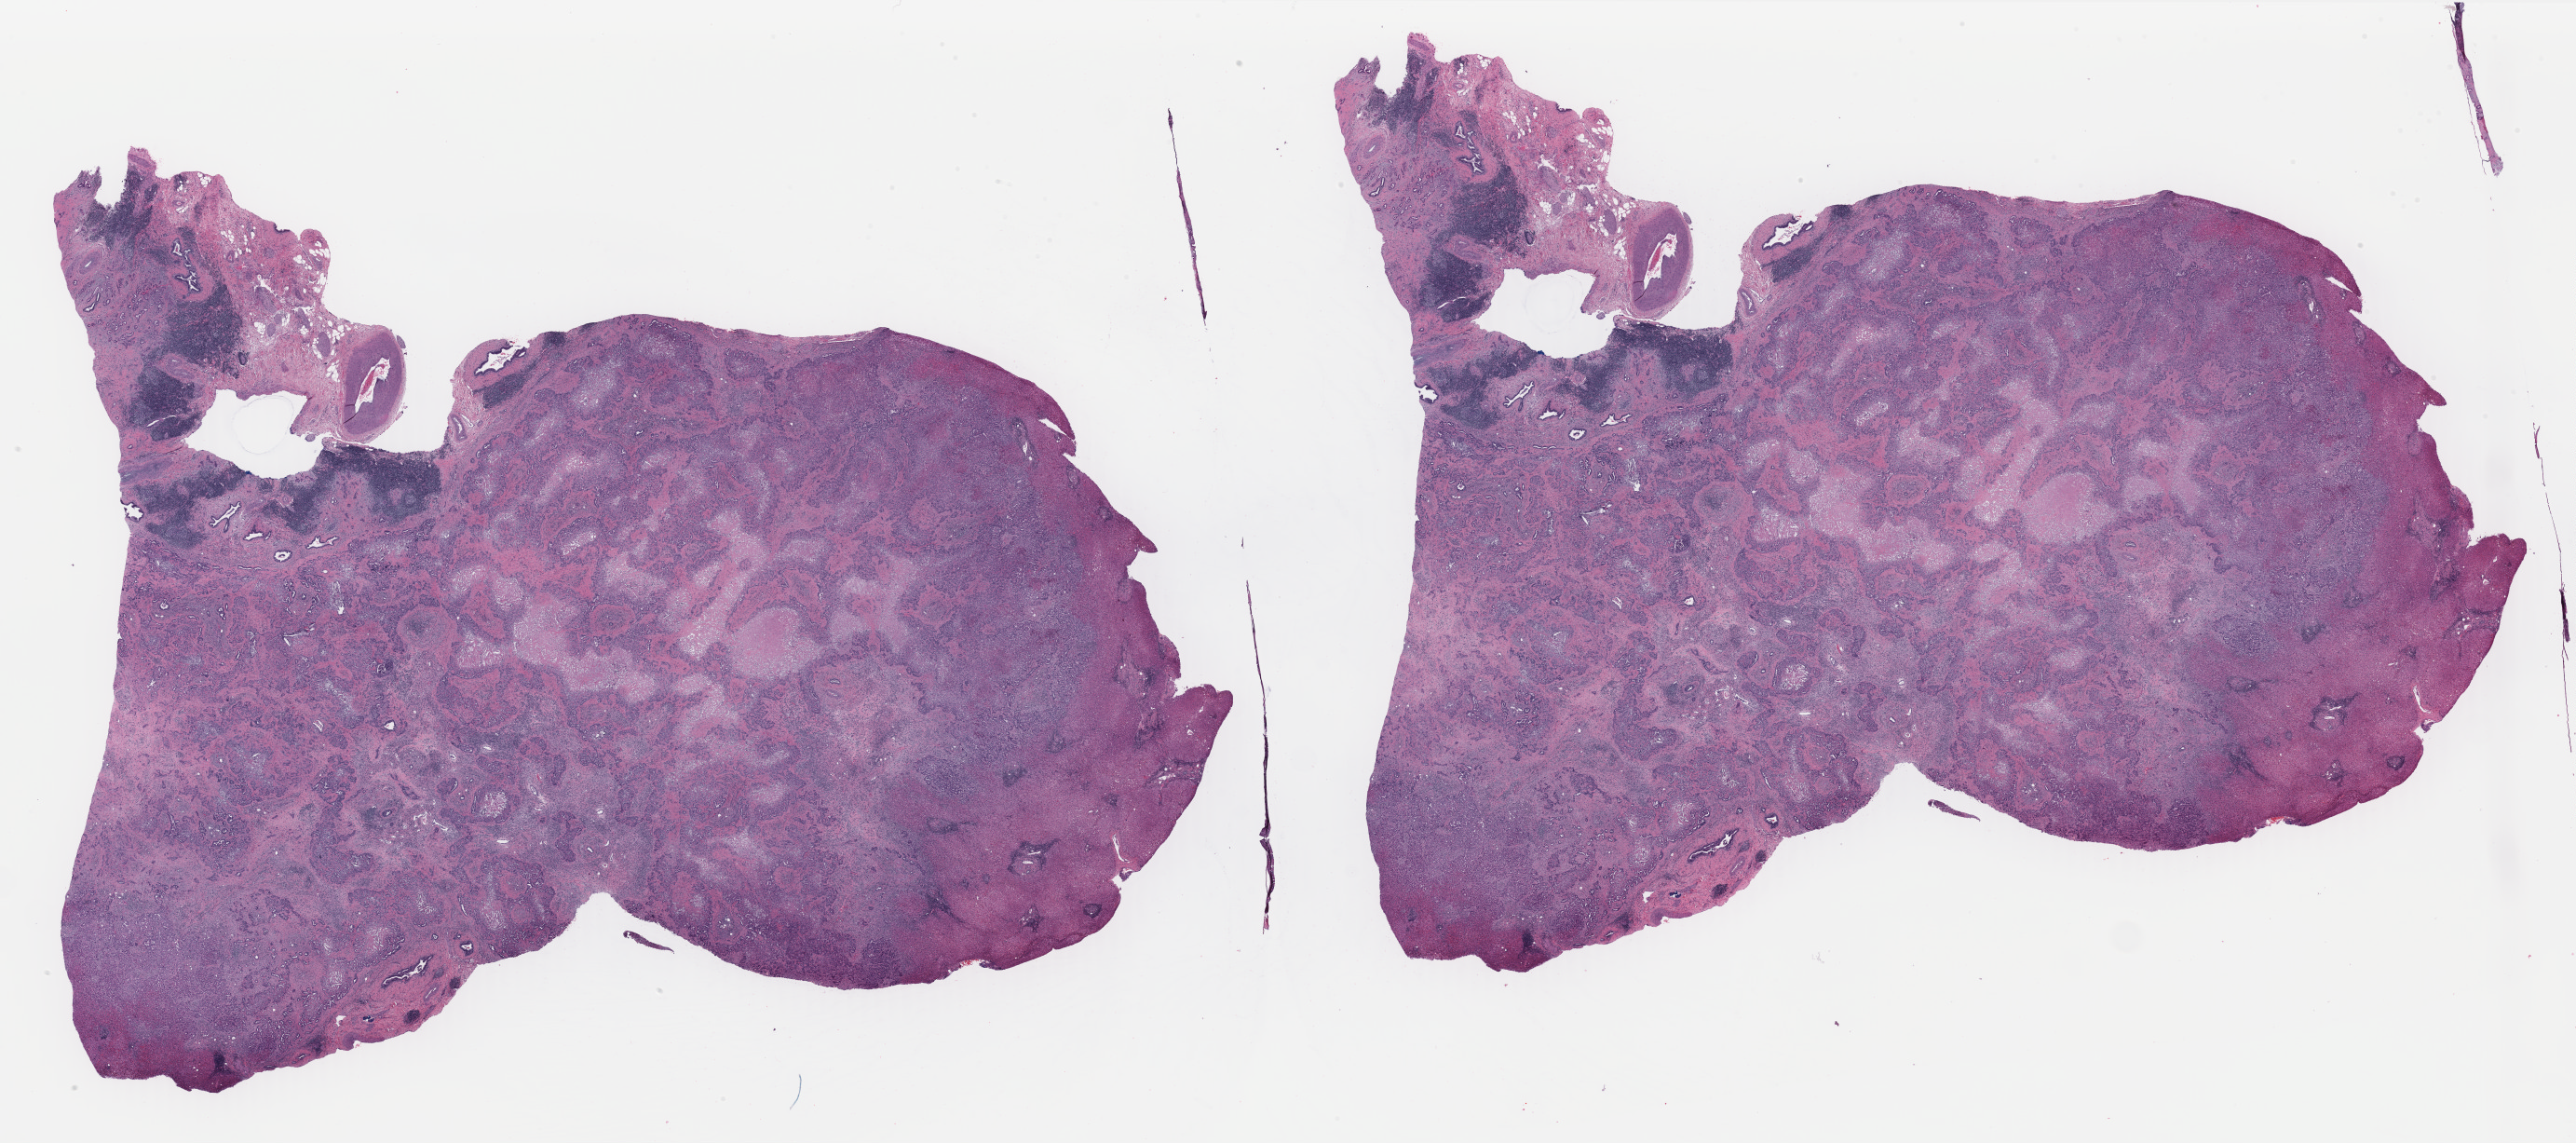
Digitized H&E-stained tissue section (whole slide) — whole scanned area (about 43.8 x 19.4 mm) shown as a low-resolution overview. Formalin-fixed paraffin-embedded (FFPE) diagnostic section. Sample: primary tumour, bile duct. Male patient; age at initial diagnosis 73 years. Histologic grade: G2 (moderately differentiated).
AJCC pathologic stage: I. Diagnosis: Cholangiocarcinoma.